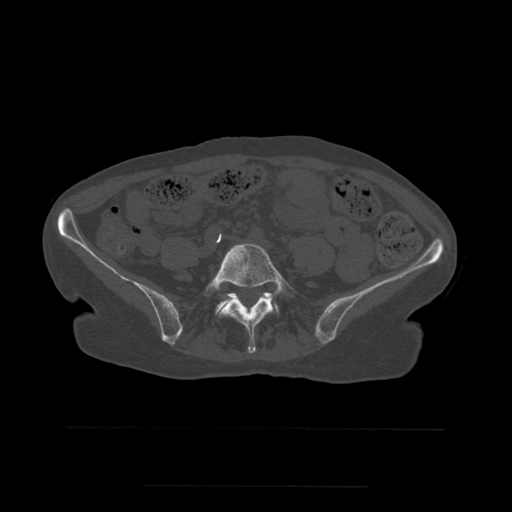
CT including the spine, one axial slice; position 144 of 544 along the scan axis; bone window (W 1800 / L 400 HU); 512 × 512 image matrix, field of view 350 × 350 mm. Patient age 58 years. Case-level facts recorded for this patient, not image findings: primary cancer: lung.
Annotated regions visible in this slice (semi-automatically segmented with operator editing):
- L5 vertebra: bounding box [x1, y1, x2, y2] px = [205, 243, 295, 354]